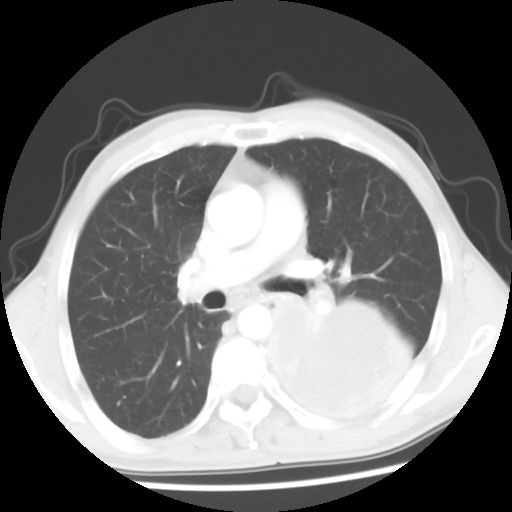
Chest CT, one axial slice; position 33 of 56 along the scan axis; reconstruction kernel STANDARD; 120 kVp; lung window (W 1500 / L -600 HU); 512 × 512 image matrix, field of view 318 × 318 mm. Patient: male, 60 years. From the clinical record (not read from this slice): clinical TNM (as recorded): T4 N0 M0.
Annotated regions visible in this slice (rectangle marked by the reading radiologist):
- lung tumour (recorded histology: squamous cell carcinoma): bounding box <257,273,420,439> (left, top, right, bottom; pixels)